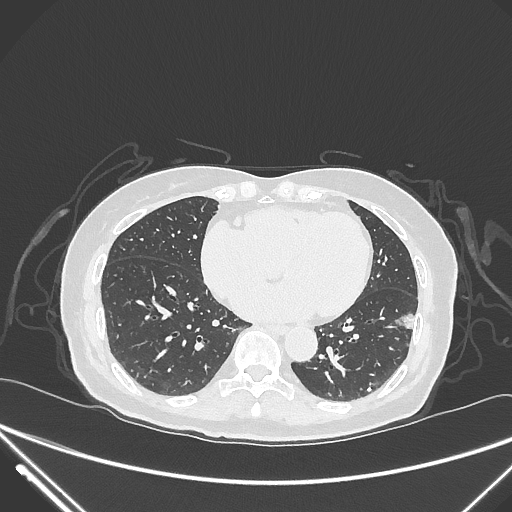
Chest CT, one axial slice; slice 115 of 310 in the series (ordered by position); reconstruction kernel IMR1,SharpPlus; 120 kVp; lung window (W 1500 / L -600 HU); 512 × 512 image matrix. Female patient, age 82 years. From the clinical record (not read from this slice): clinical TNM (as recorded): T1c N0 M0; histopathological grade: G2.
Outlined on this slice (rectangle marked by the reading radiologist):
- lung tumour (recorded histology: adenocarcinoma): bounding box (x1, y1, x2, y2) in pixels: (393, 307, 419, 340)